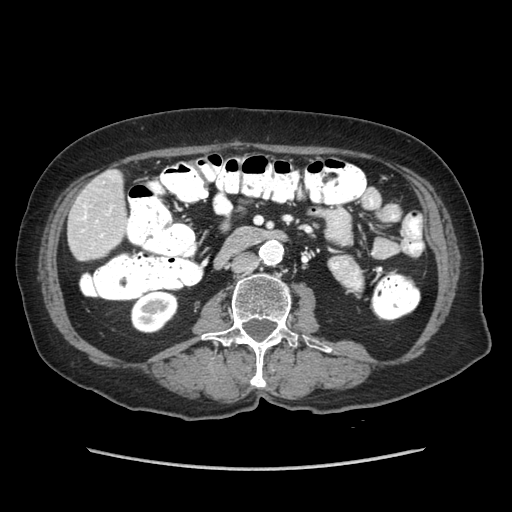
Contrast-enhanced abdominal CT (liver protocol), one axial slice. Position 12 of 89 along the scan axis. Reconstruction kernel STANDARD. Soft-tissue window (W 400 / L 40 HU). 512 × 512 image matrix, field of view 360 × 360 mm. From the clinical record (not read from this slice): diagnosis: hepatocellular carcinoma (patient treated with transarterial chemoembolisation; whether this scan precedes or follows treatment is not stated here); TNM stage (as recorded): Stage-IIIA.
Outlined on this slice (semi-automatically segmented with operator editing):
- liver parenchyma outside the tumour (the mass and vessels are separate outlines, so this box may not span the whole liver): bounding box (x1, y1, x2, y2) in pixels: (68, 170, 126, 260)
- liver vessels: (83, 214, 103, 237)